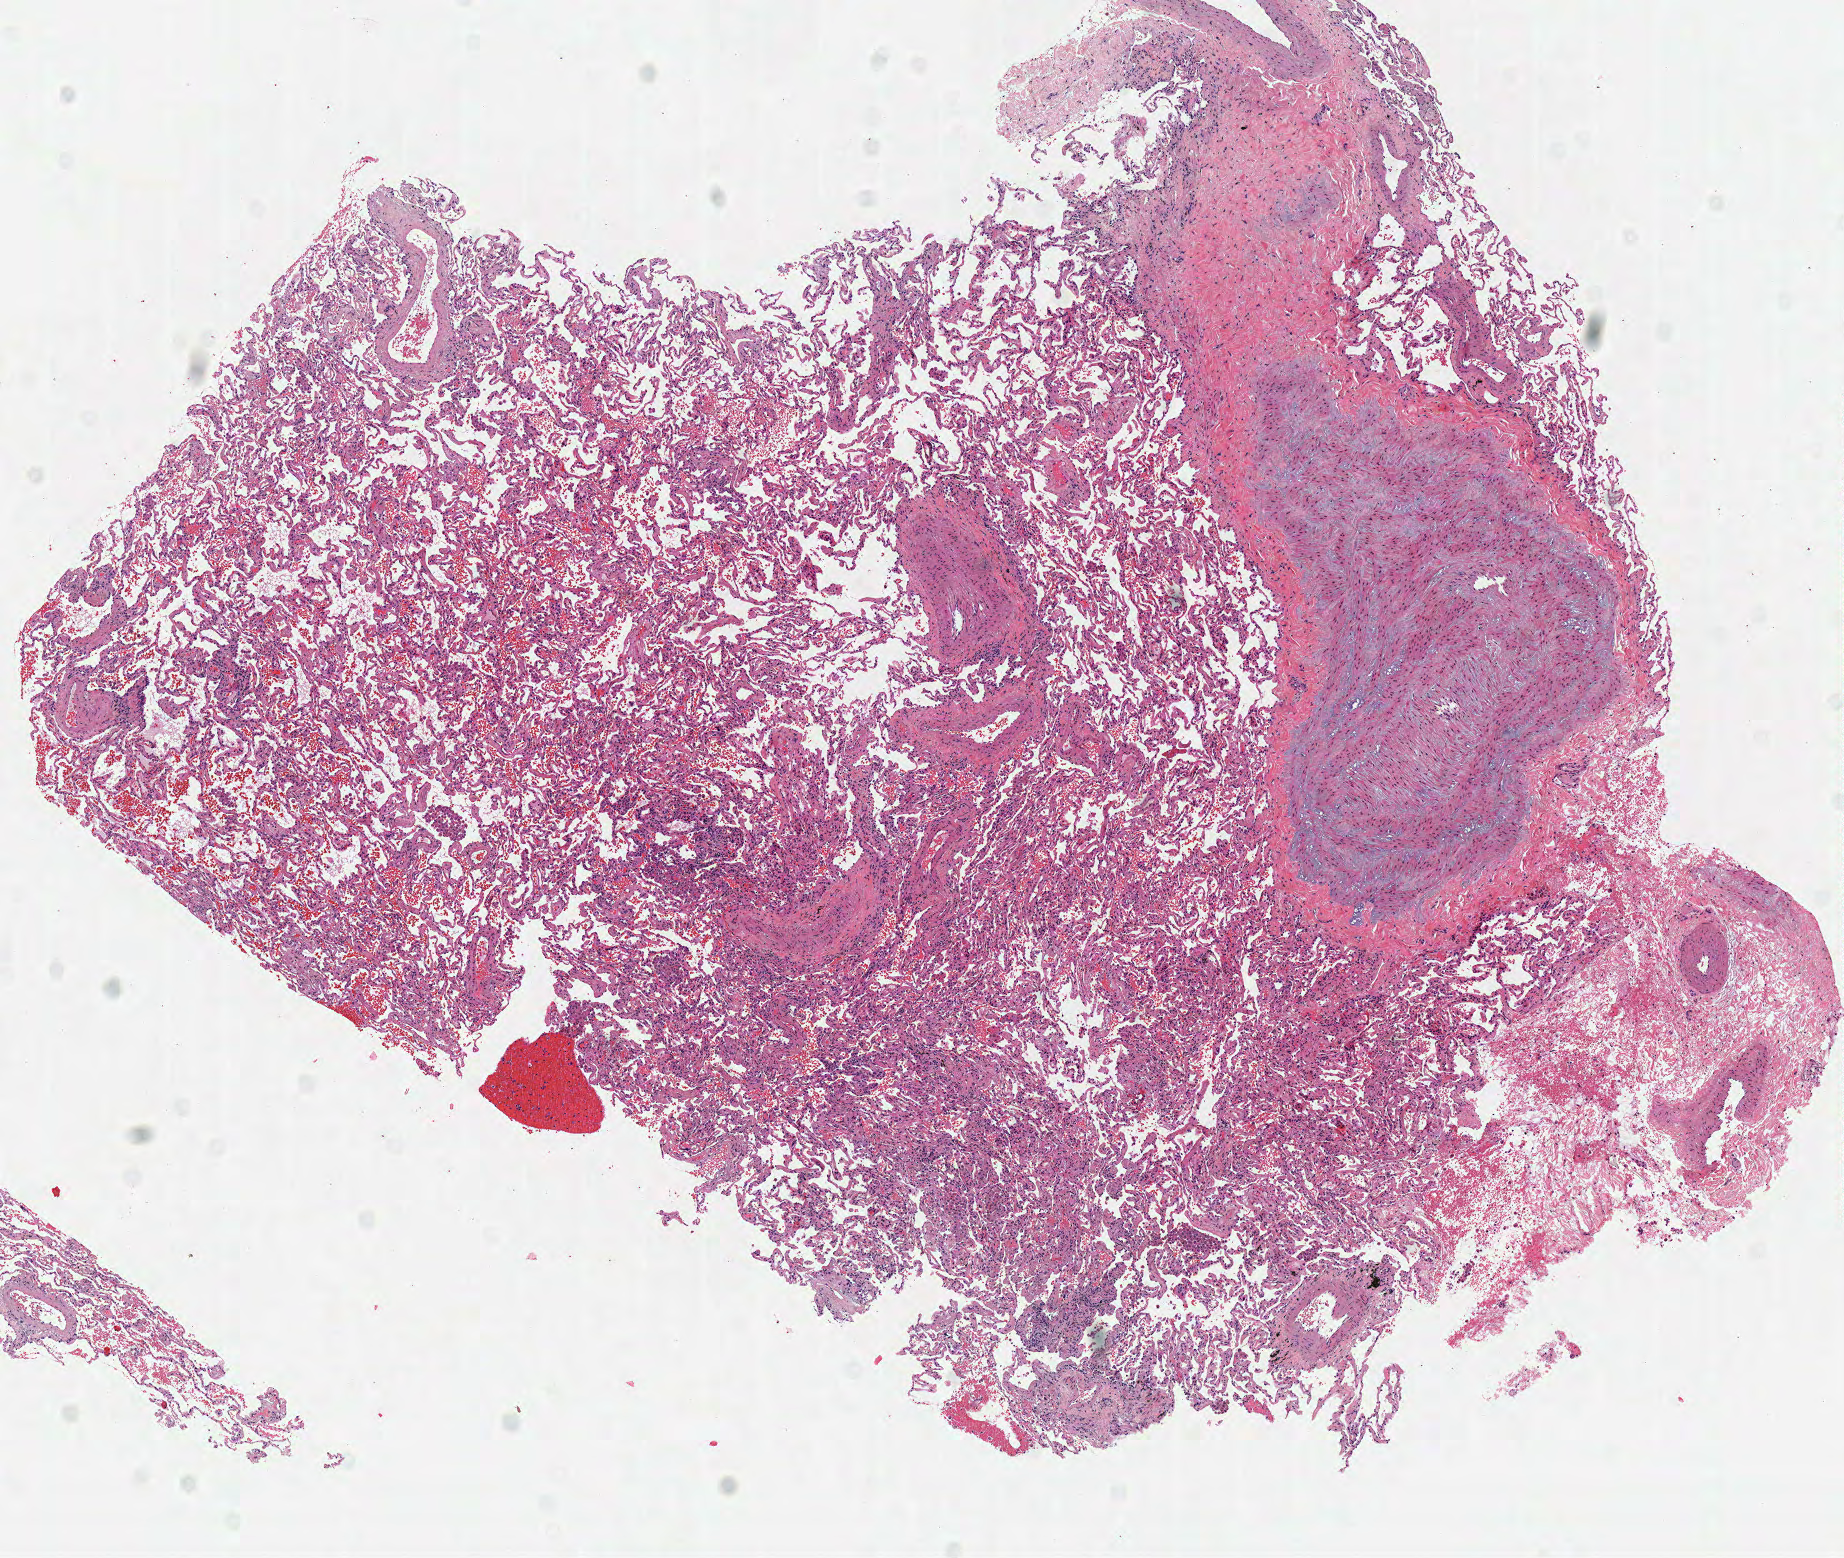
Whole-slide histology image, H&E — whole scanned area (about 7.3 x 6.1 mm, acquisition: 40x scan) shown as a low-resolution overview, frozen section from the top of the tissue portion, sample: solid tissue normal (non-tumour tissue), lung. Male patient; age at initial diagnosis 70 years.
This section: solid tissue normal (non-tumour) sample from the same patient. Patient diagnosis: Adenocarcinoma, NOS.